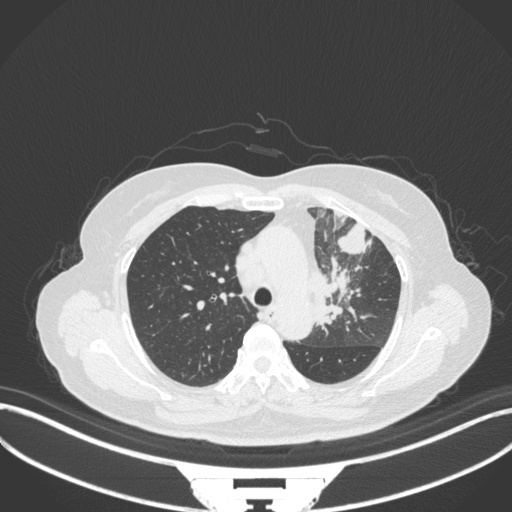
Chest CT, one axial slice; slice 240 of 382 in the series (ordered by position); reconstruction kernel B31f; 120 kVp; lung window (W 1500 / L -600 HU); 1 mm slice thickness; 512 × 512 image matrix, field of view 400 × 400 mm. Female patient, age 64 years. Case-level facts recorded for this patient, not image findings: clinical TNM (as recorded): T2a N2 M0.
Annotated regions visible in this slice (rectangle marked by the reading radiologist):
- lung tumour (recorded histology: adenocarcinoma): bounding box [x1, y1, x2, y2] px = [310, 251, 360, 332]
- lung tumour (recorded histology: adenocarcinoma): [337, 218, 373, 257]